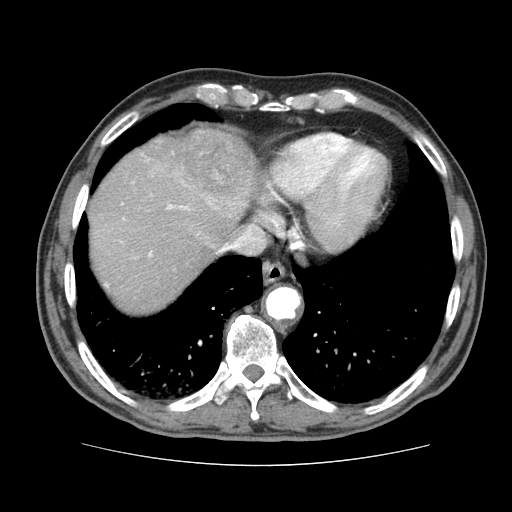
Contrast-enhanced abdominal CT (liver protocol), one axial slice. Slice 68 of 79 in the series (ordered by position). 120 kVp. Soft-tissue window (W 400 / L 40 HU). 2.5 mm slice thickness. 512 × 512 image matrix, field of view 360 × 360 mm. Case-level facts recorded for this patient, not image findings: diagnosis: hepatocellular carcinoma (patient treated with transarterial chemoembolisation; whether this scan precedes or follows treatment is not stated here); TNM stage (as recorded): Stage-I; Child-Pugh class: A; tumour nodularity: uninodular.
Structures marked on this image (semi-automatically segmented with operator editing):
- abdominal aorta: bounding box <267,288,299,318> (left, top, right, bottom; pixels)
- liver parenchyma outside the tumour (the mass and vessels are separate outlines, so this box may not span the whole liver): <88,128,248,312>
- mass: <156,129,262,220>
- liver vessels: <106,204,189,287>